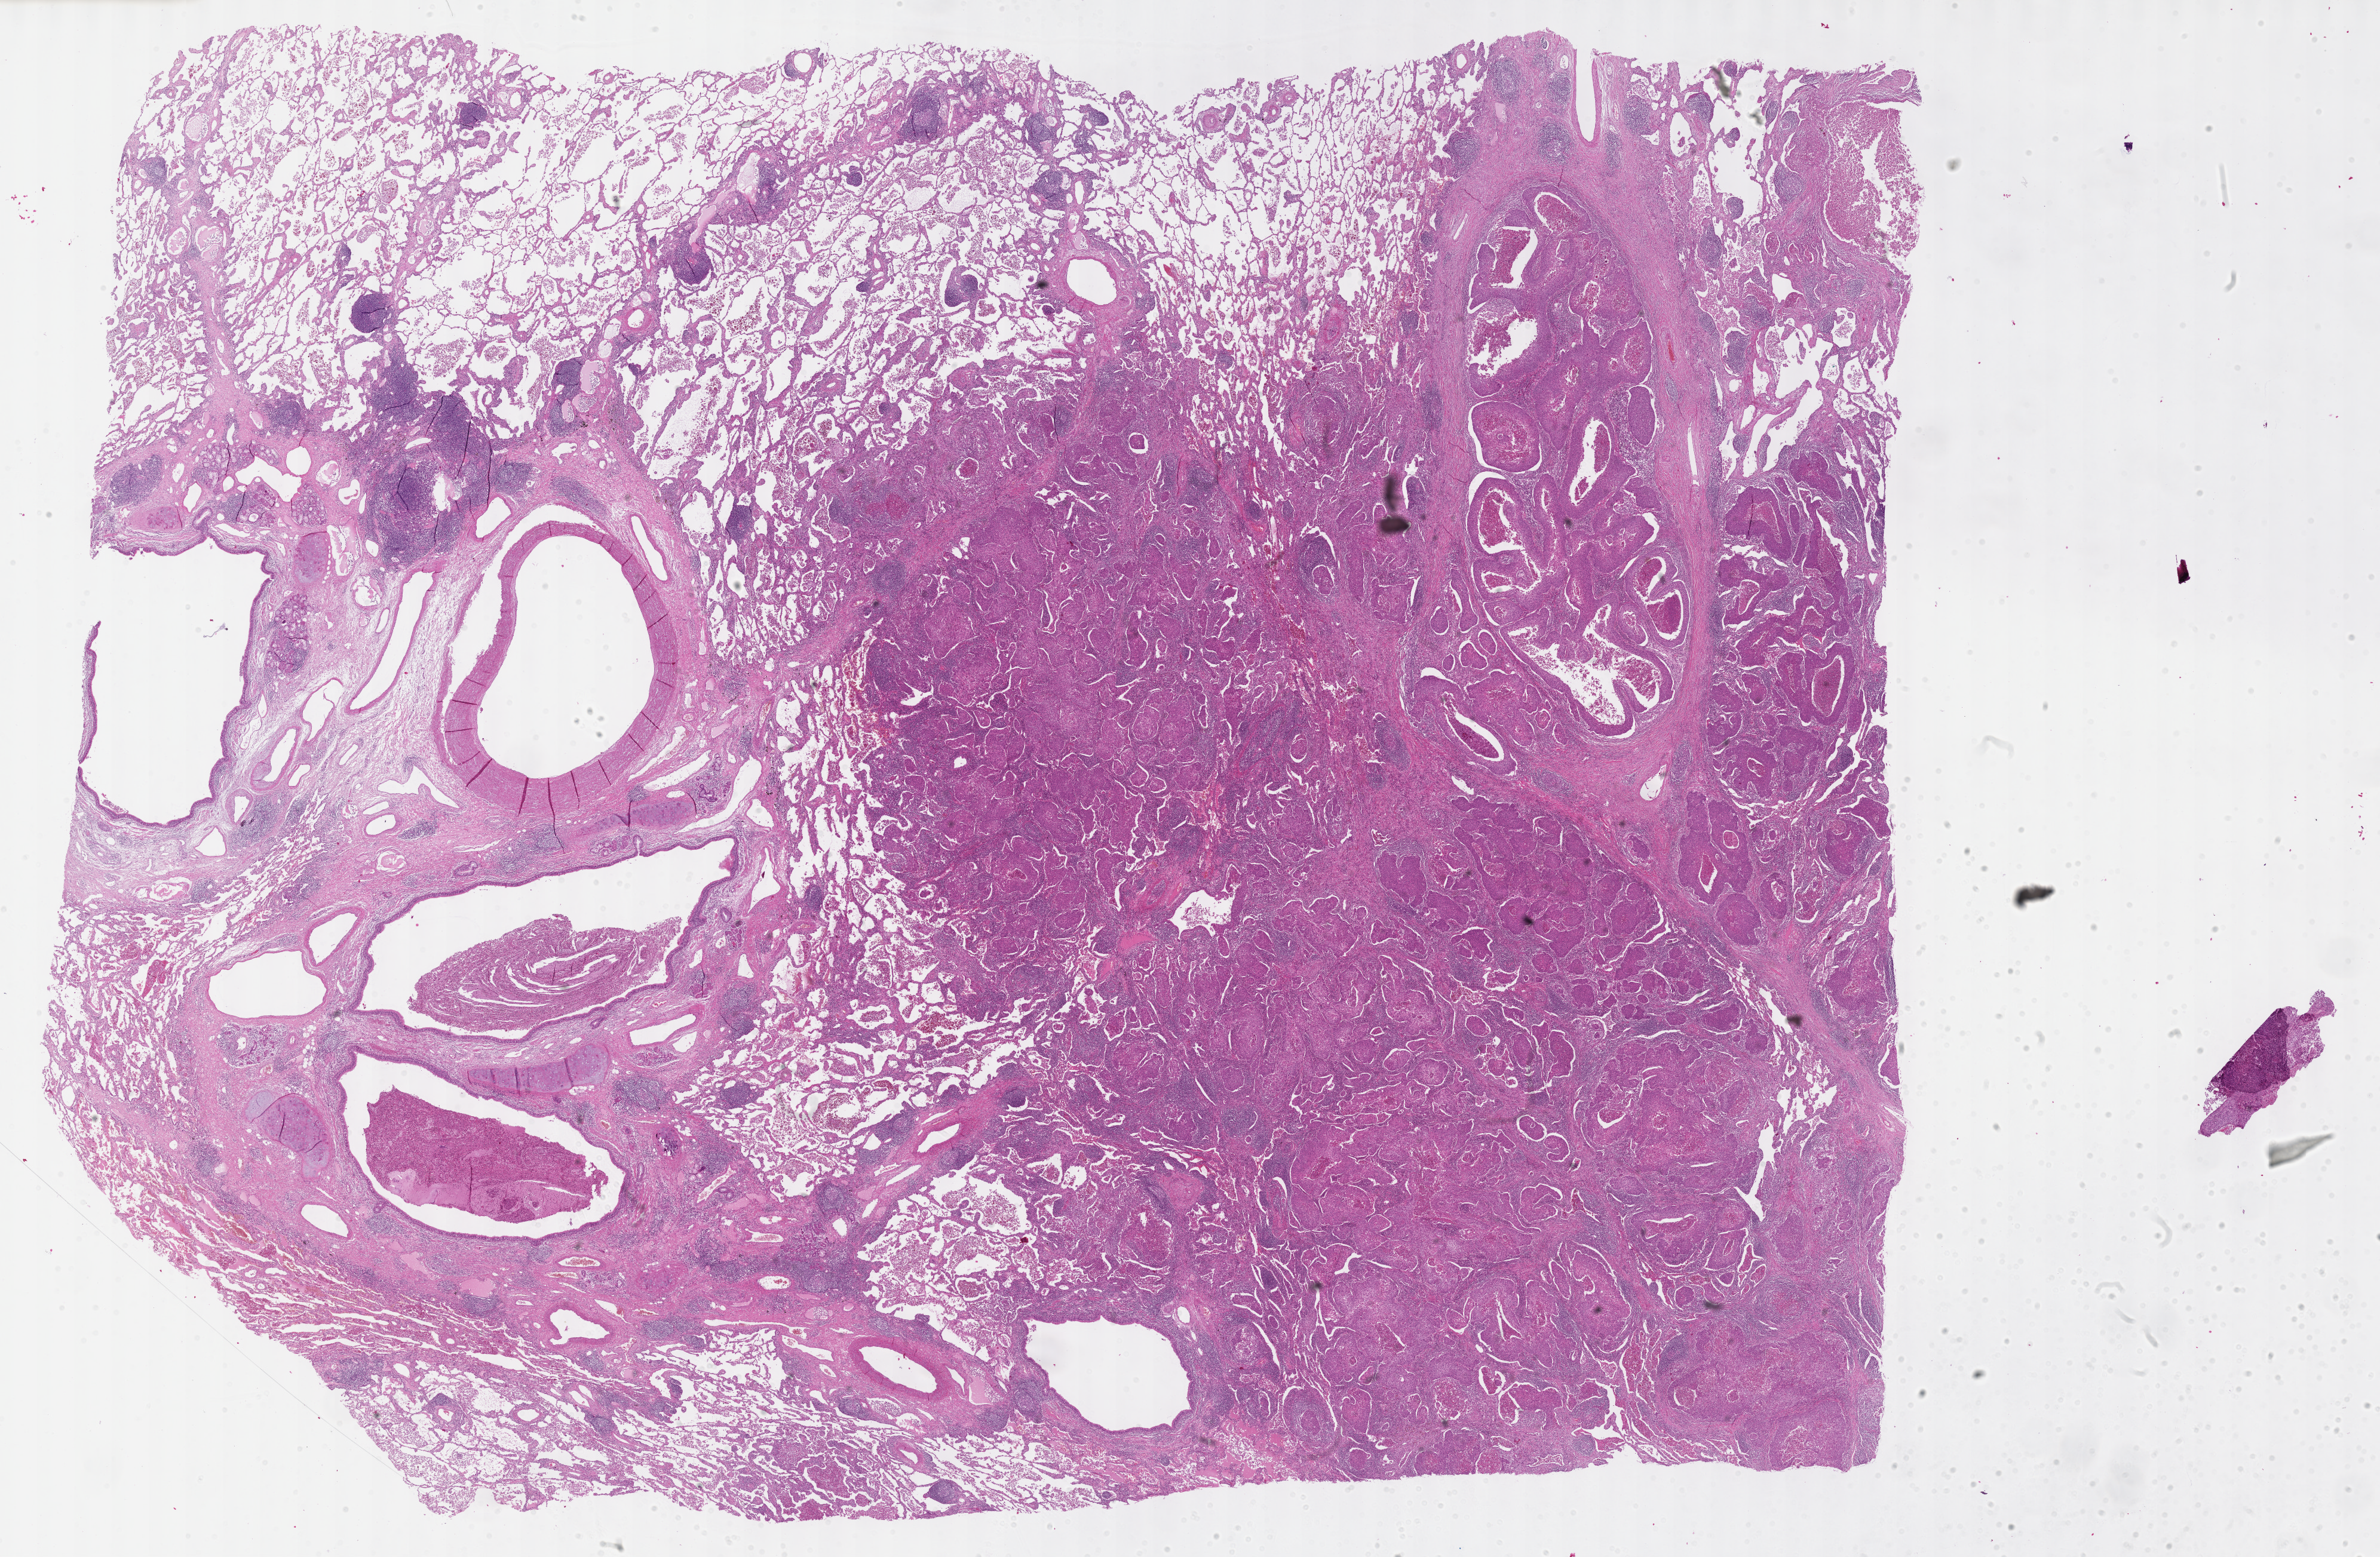
Hematoxylin and eosin (H&E) stained whole-slide image — a low-resolution overview of the entire scanned area, about 32.2 x 21.1 mm (slide scanned at 40x); formalin-fixed paraffin-embedded (FFPE) diagnostic section; primary tumour sample from the lung. Female, age 70 years at initial diagnosis.
Histologic diagnosis: Squamous cell carcinoma, keratinizing, NOS (upper lobe, lung). AJCC pathologic stage: IIIA (7th edition). Laterality: left.